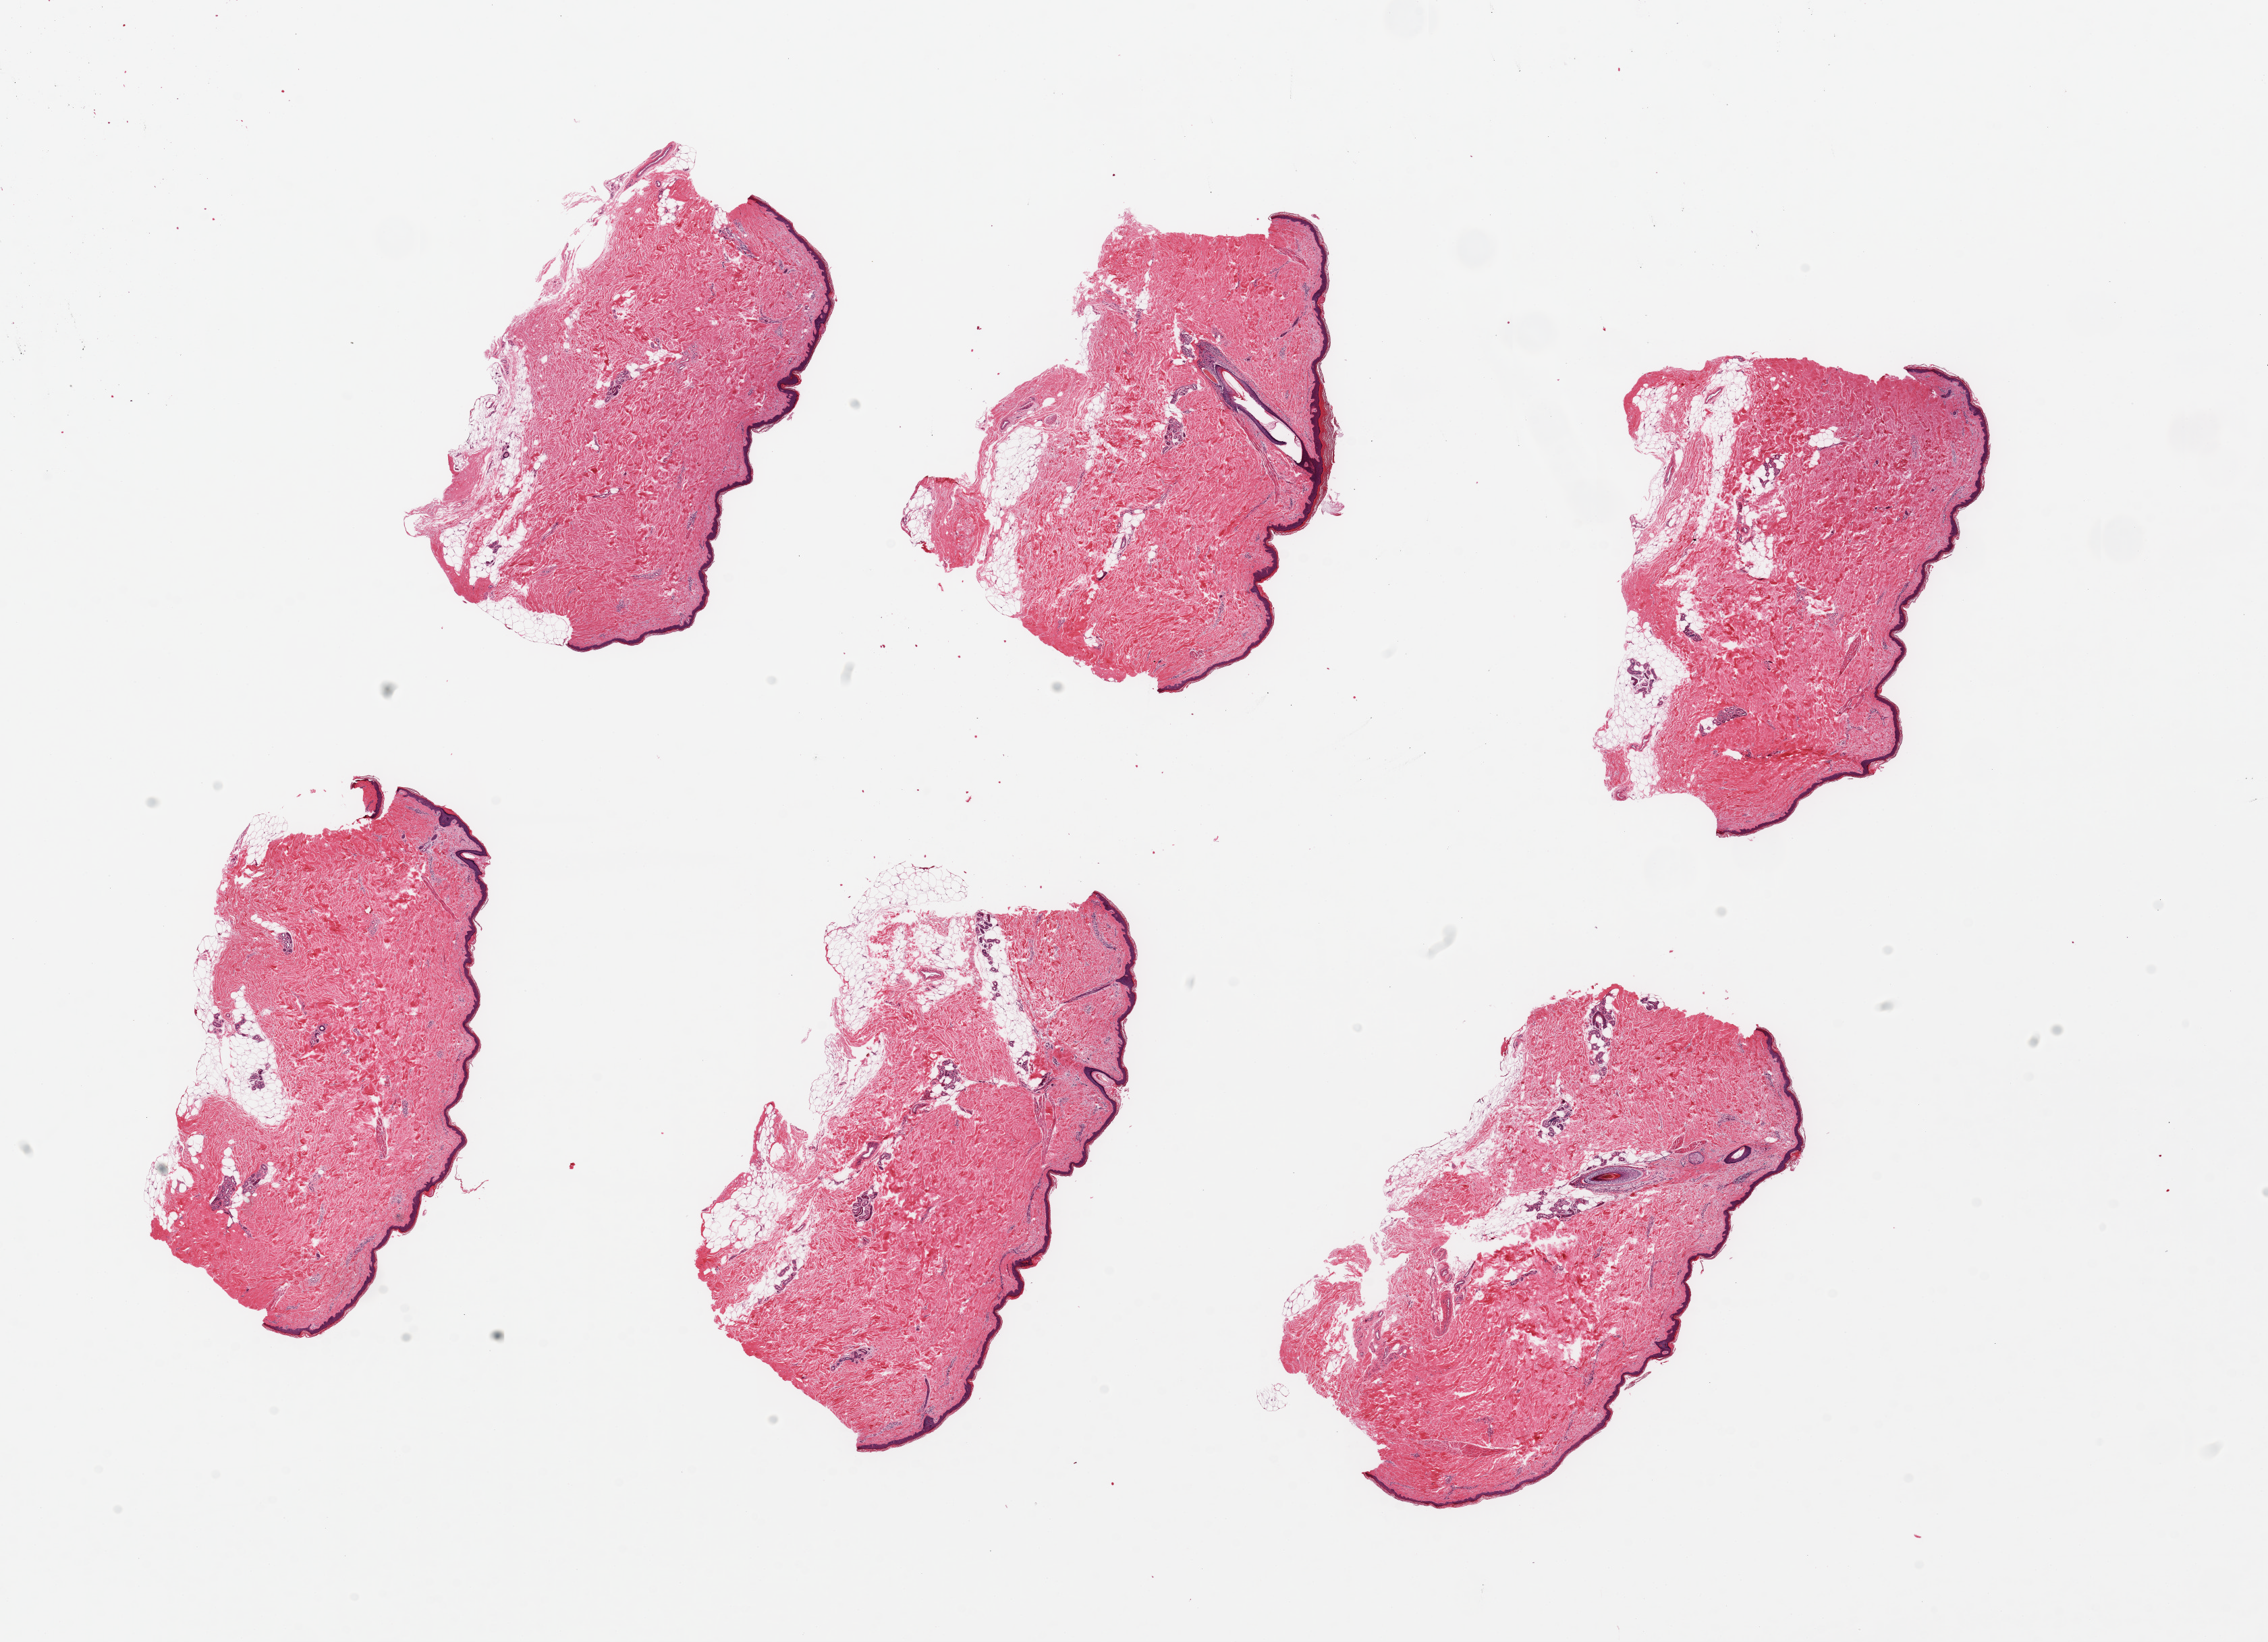
Digitized haematoxylin and eosin-stained section, low-resolution overview of the scanned area, about 26.6 x 19.2 mm. PAXgene-fixed, paraffin-embedded tissue. Section of skin of lower leg (target tissue). Donor tissue sample.
• reviewer comment on this tissue sample: 6 pieces ~6x3mm. Squamous epithelium is ~1% thickness